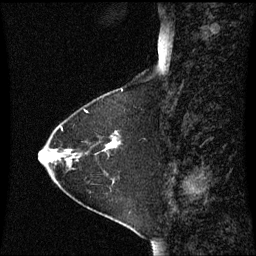
Breast MRI (dynamic contrast-enhanced), one sagittal slice; slice 19 of 60 in the series (ordered by position); dynamic contrast-enhanced series, image 2 of 3 at this slice position (ordered by acquisition); 1.5 T; TE 4.2 ms, TR 8.9 ms; 2 mm slice thickness; 256 × 256 image matrix, field of view 210 × 210 mm. Patient: female, 63 years. From the clinical record (not read from this slice): setting: breast cancer imaged before/during neoadjuvant chemotherapy; receptor status: HR-positive, HER2-negative.
Structures marked on this image (semi-automatically segmented with operator editing):
- analysis volume of interest (the breast-tissue region the enhancement analysis was run in; not a lesion): bounding box <88,132,122,156> (left, top, right, bottom; pixels)
- tumour enhancement mask (voxels above the 70 % enhancement threshold inside the analysis volume of interest): <107,139,120,149>